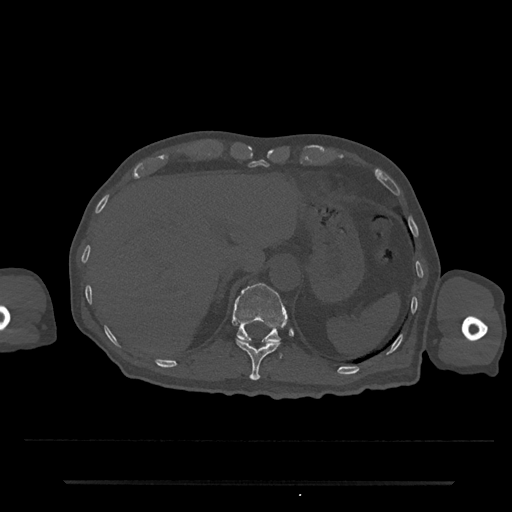
CT including the spine, one axial slice. Position 229 of 797 along the scan axis. Bone window (W 1800 / L 400 HU). 0.5 mm slice thickness. 512 × 512 image matrix, field of view 427 × 427 mm. Patient: male, 74 years. Case-level facts recorded for this patient, not image findings: primary cancer: prostate.
Annotated regions visible in this slice (semi-automatically segmented with operator editing):
- T11 vertebra: bounding box (x1, y1, x2, y2) in pixels: (236, 339, 280, 381)
- T12 vertebra: (233, 283, 287, 343)